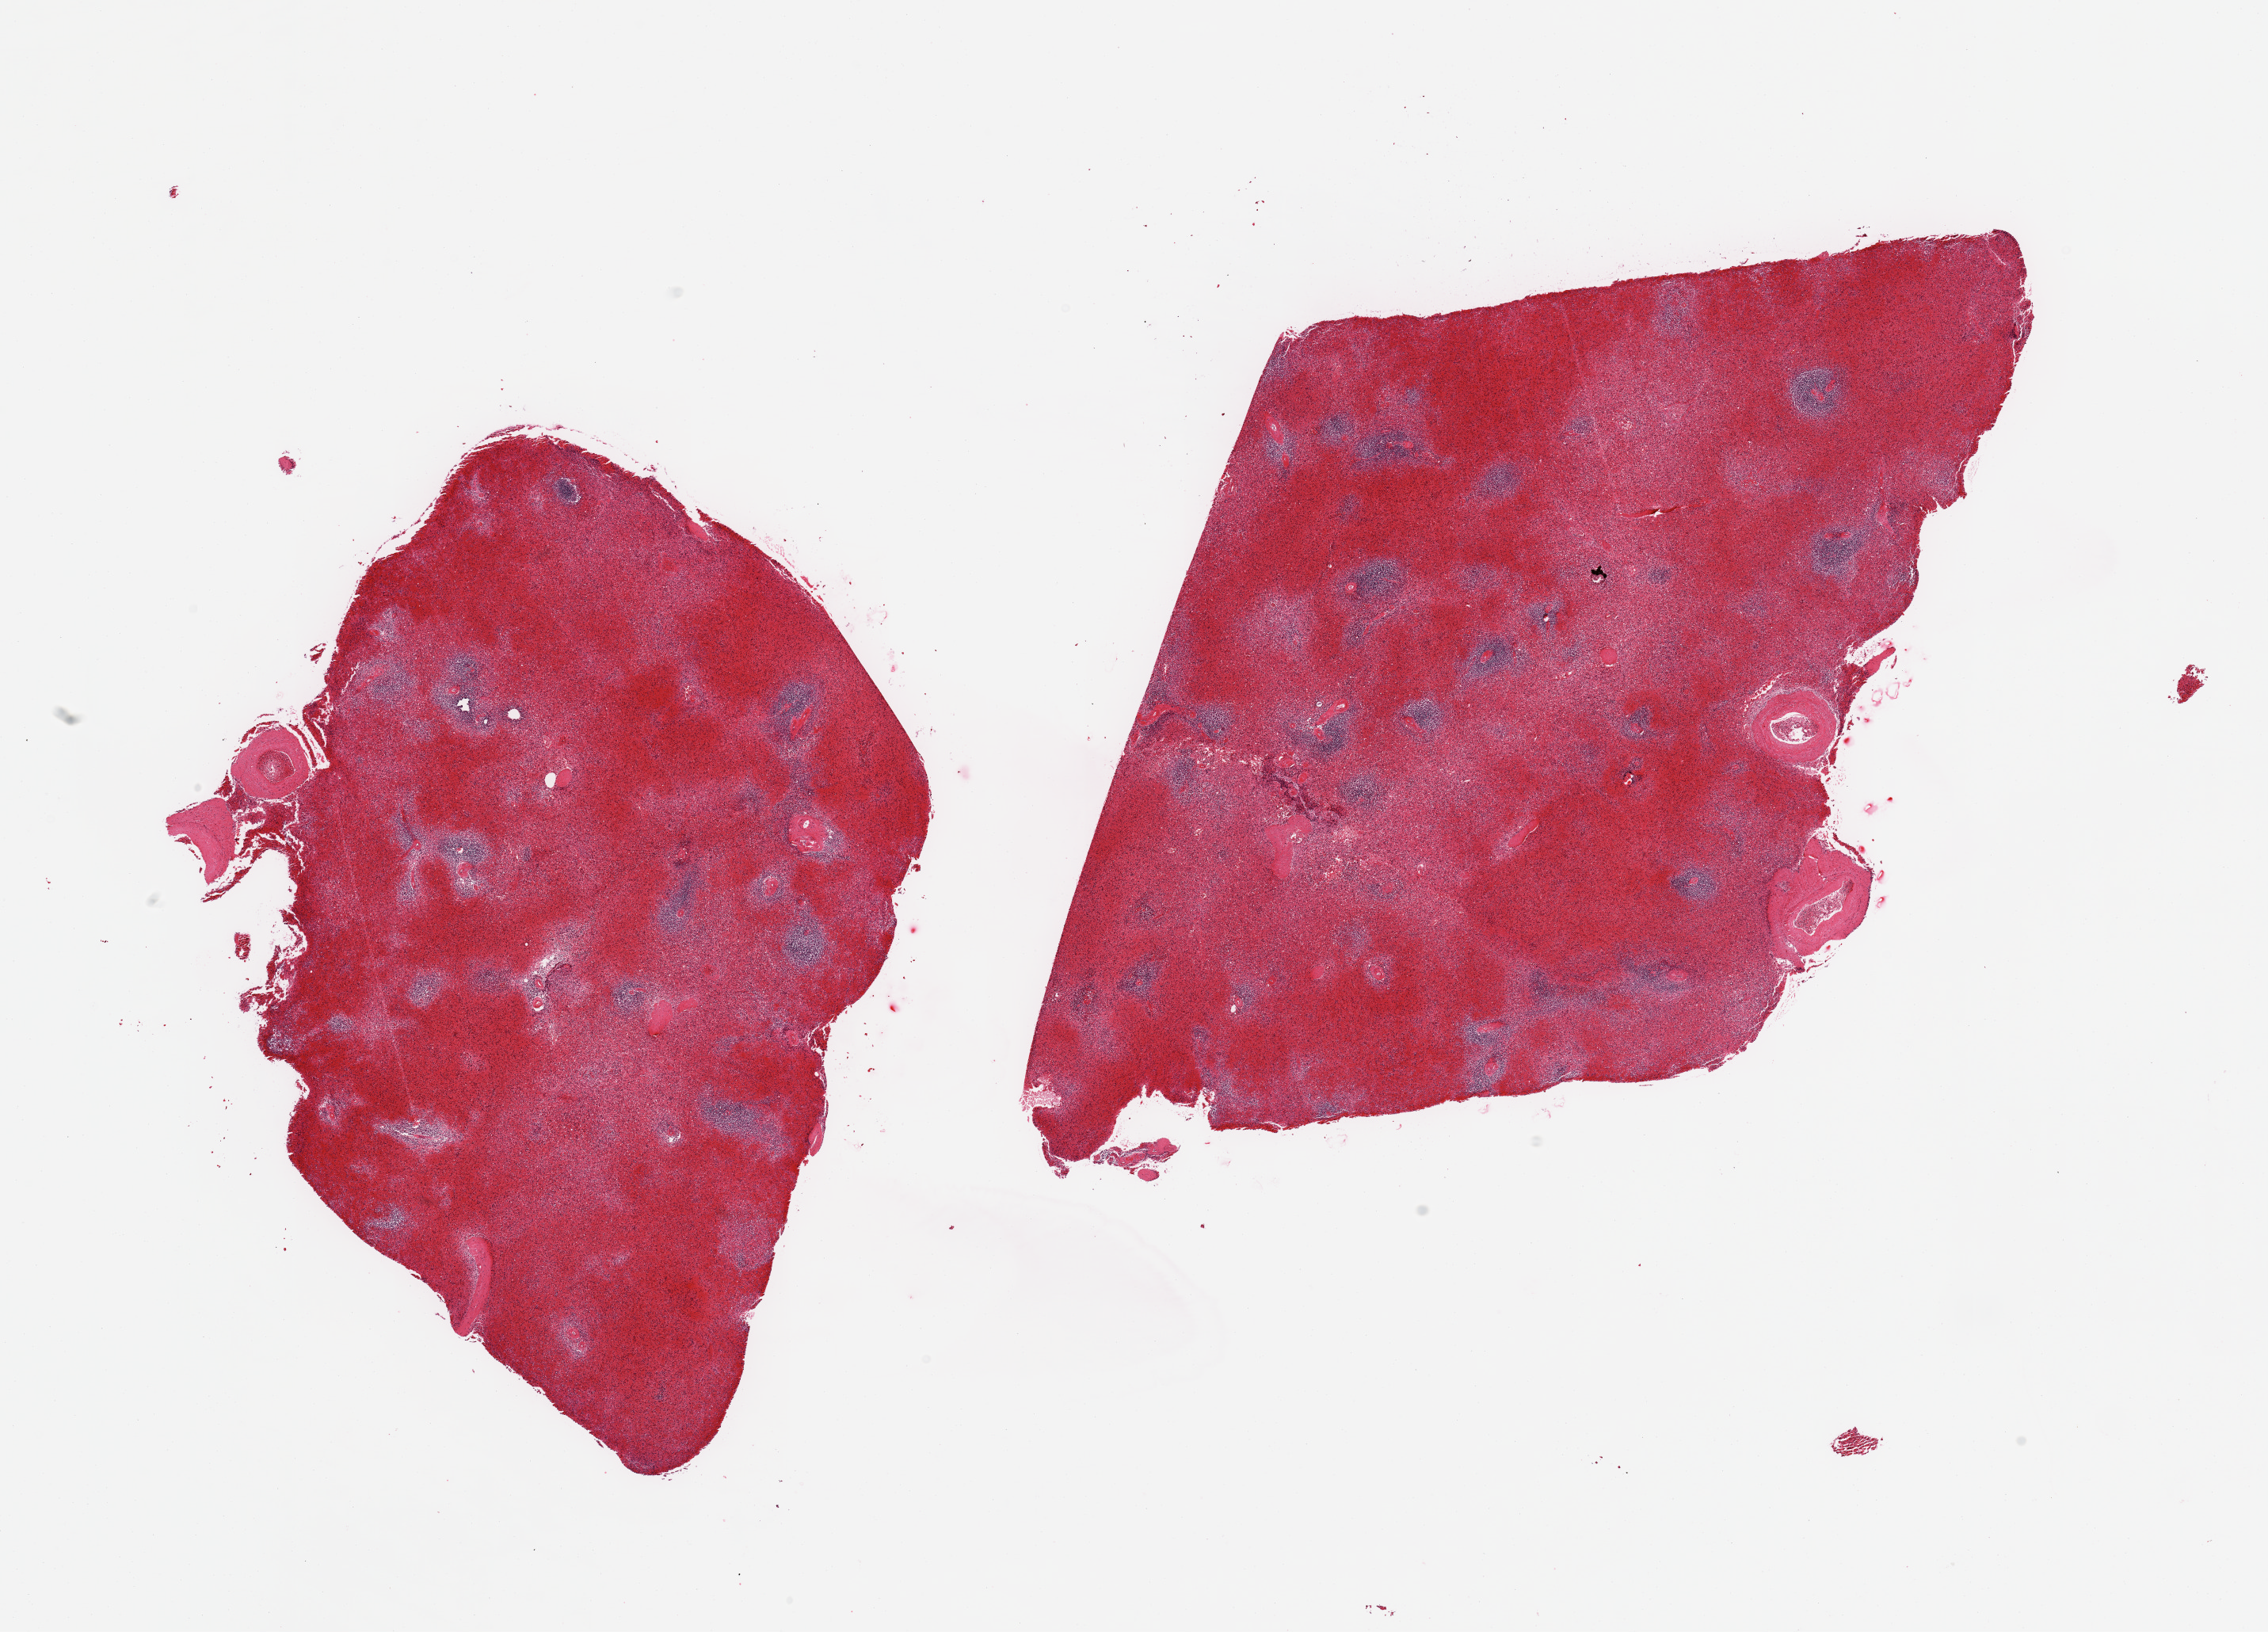
Whole-slide image, hematoxylin and eosin (H&E) stain, brightfield, low-resolution overview of the scanned area, about 22.6 x 16.3 mm. PAXgene-fixed, paraffin-embedded tissue. Section of spleen (target tissue). Donor tissue sample. Donor: male.
Reviewer comment on this tissue sample: 2 pieces; moderate red pulp congestion.